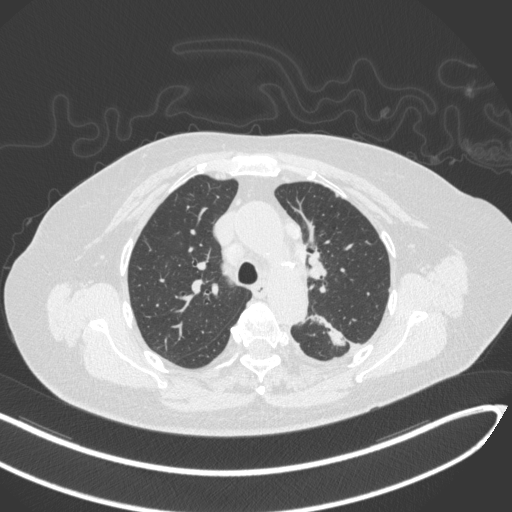
Chest CT, one axial slice; 120 kVp; lung window (W 1500 / L -600 HU); 512 × 512 image matrix. Patient: female, 76 years. From the clinical record (not read from this slice): clinical TNM (as recorded): T1c N0 M0.
Outlined on this slice (bounding box drawn by a radiologist):
- lung tumour (recorded histology: adenocarcinoma): bounding box (x1, y1, x2, y2) in pixels: (308, 309, 358, 353)